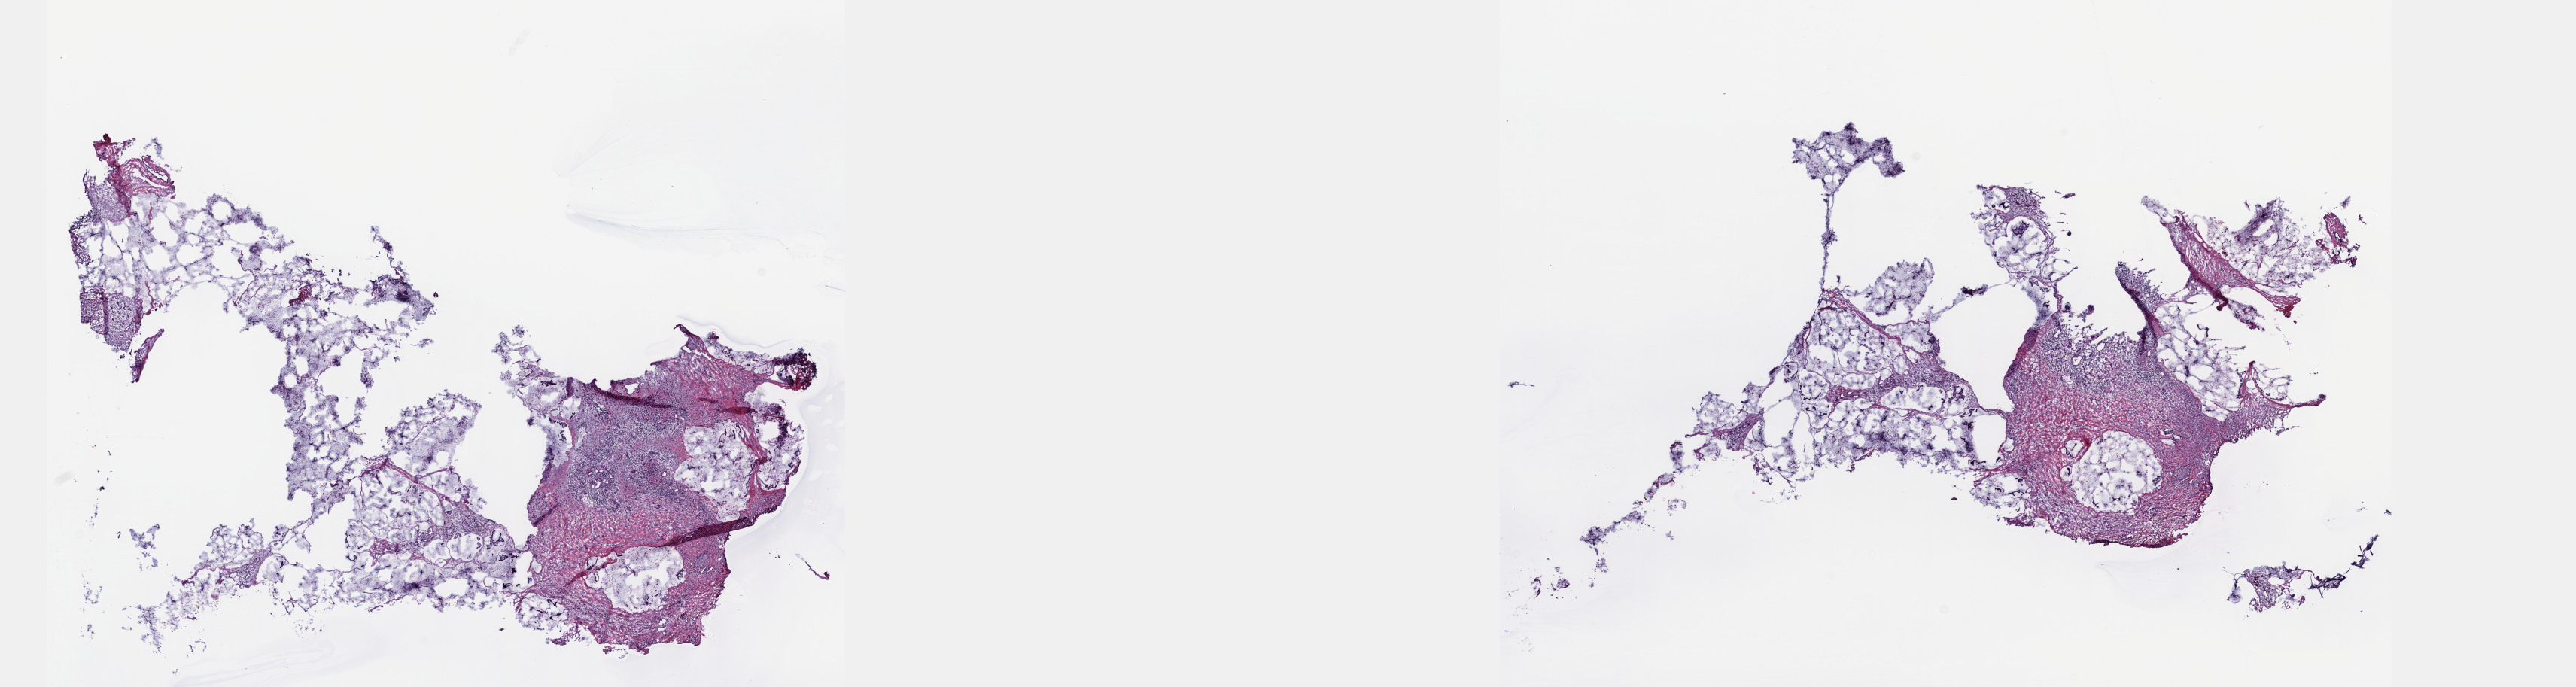
Whole-slide histology image, H&E-stained, shown as a low-resolution overview of the whole scanned area (about 27.7 x 7.4 mm, from a 40x scan). Frozen section. Pancreas, primary tumour sample. Male, age 65 years at initial diagnosis. Histologic grade: G1 (well differentiated). Slide review estimates, as recorded: tumour cells 100%, tumour nuclei 20%, normal cells 0%, stromal cells 0%, necrosis 0%. Inflammatory infiltration, as recorded: lymphocyte infiltration 10%, monocyte infiltration 3%, neutrophil infiltration 0%.
Pathologic diagnosis: Mucinous adenocarcinoma (head of pancreas). Lymph nodes positive (case pathology): 7 of 11 examined. AJCC pathologic stage: IIB.